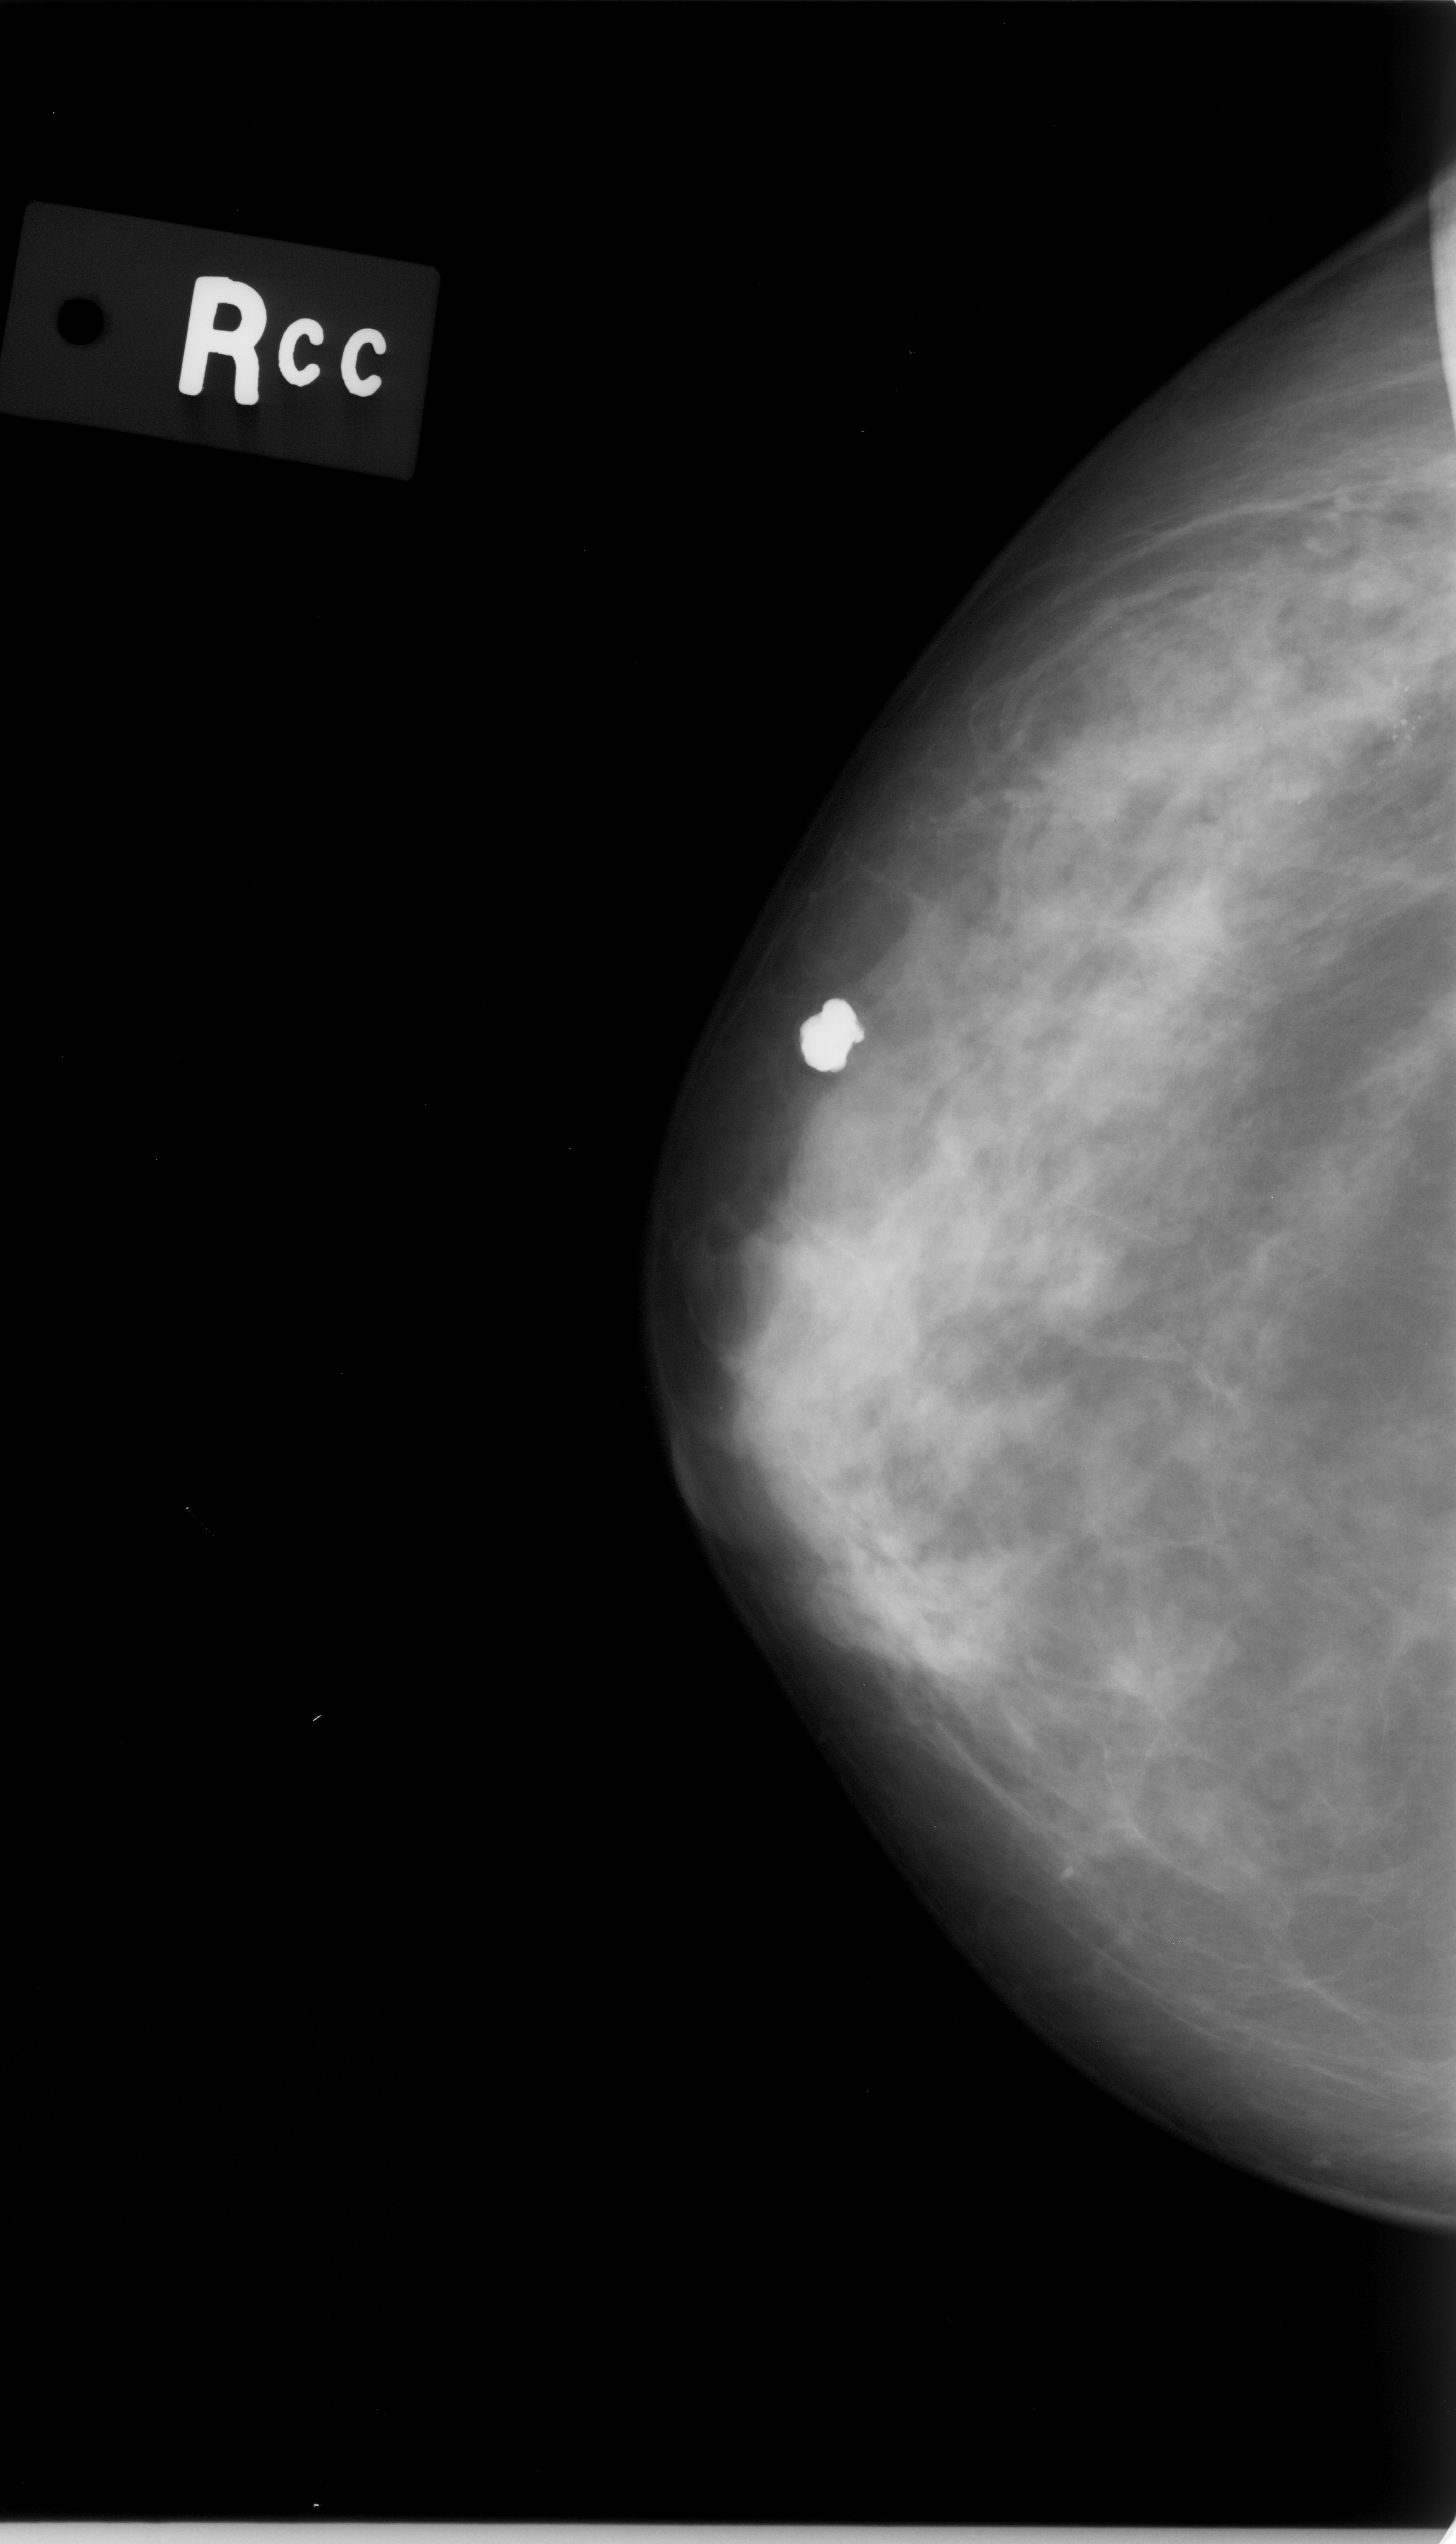
Scanned film-screen mammogram. Right breast. Craniocaudal (CC) view. Breast composition: heterogeneously dense (BI-RADS density category 3 of 4). 1456 × 2544 image matrix.
Expert-marked regions of interest on this image (one box per marked abnormality):
- calcifications, morphology pleomorphic, distribution clustered; BI-RADS assessment category 5; subtlety rating 4 on a 1 (subtle) to 5 (obvious) scale; pathology result (as recorded, not read from the image): malignant: box from (x=1306, y=622) to (x=1440, y=826) px